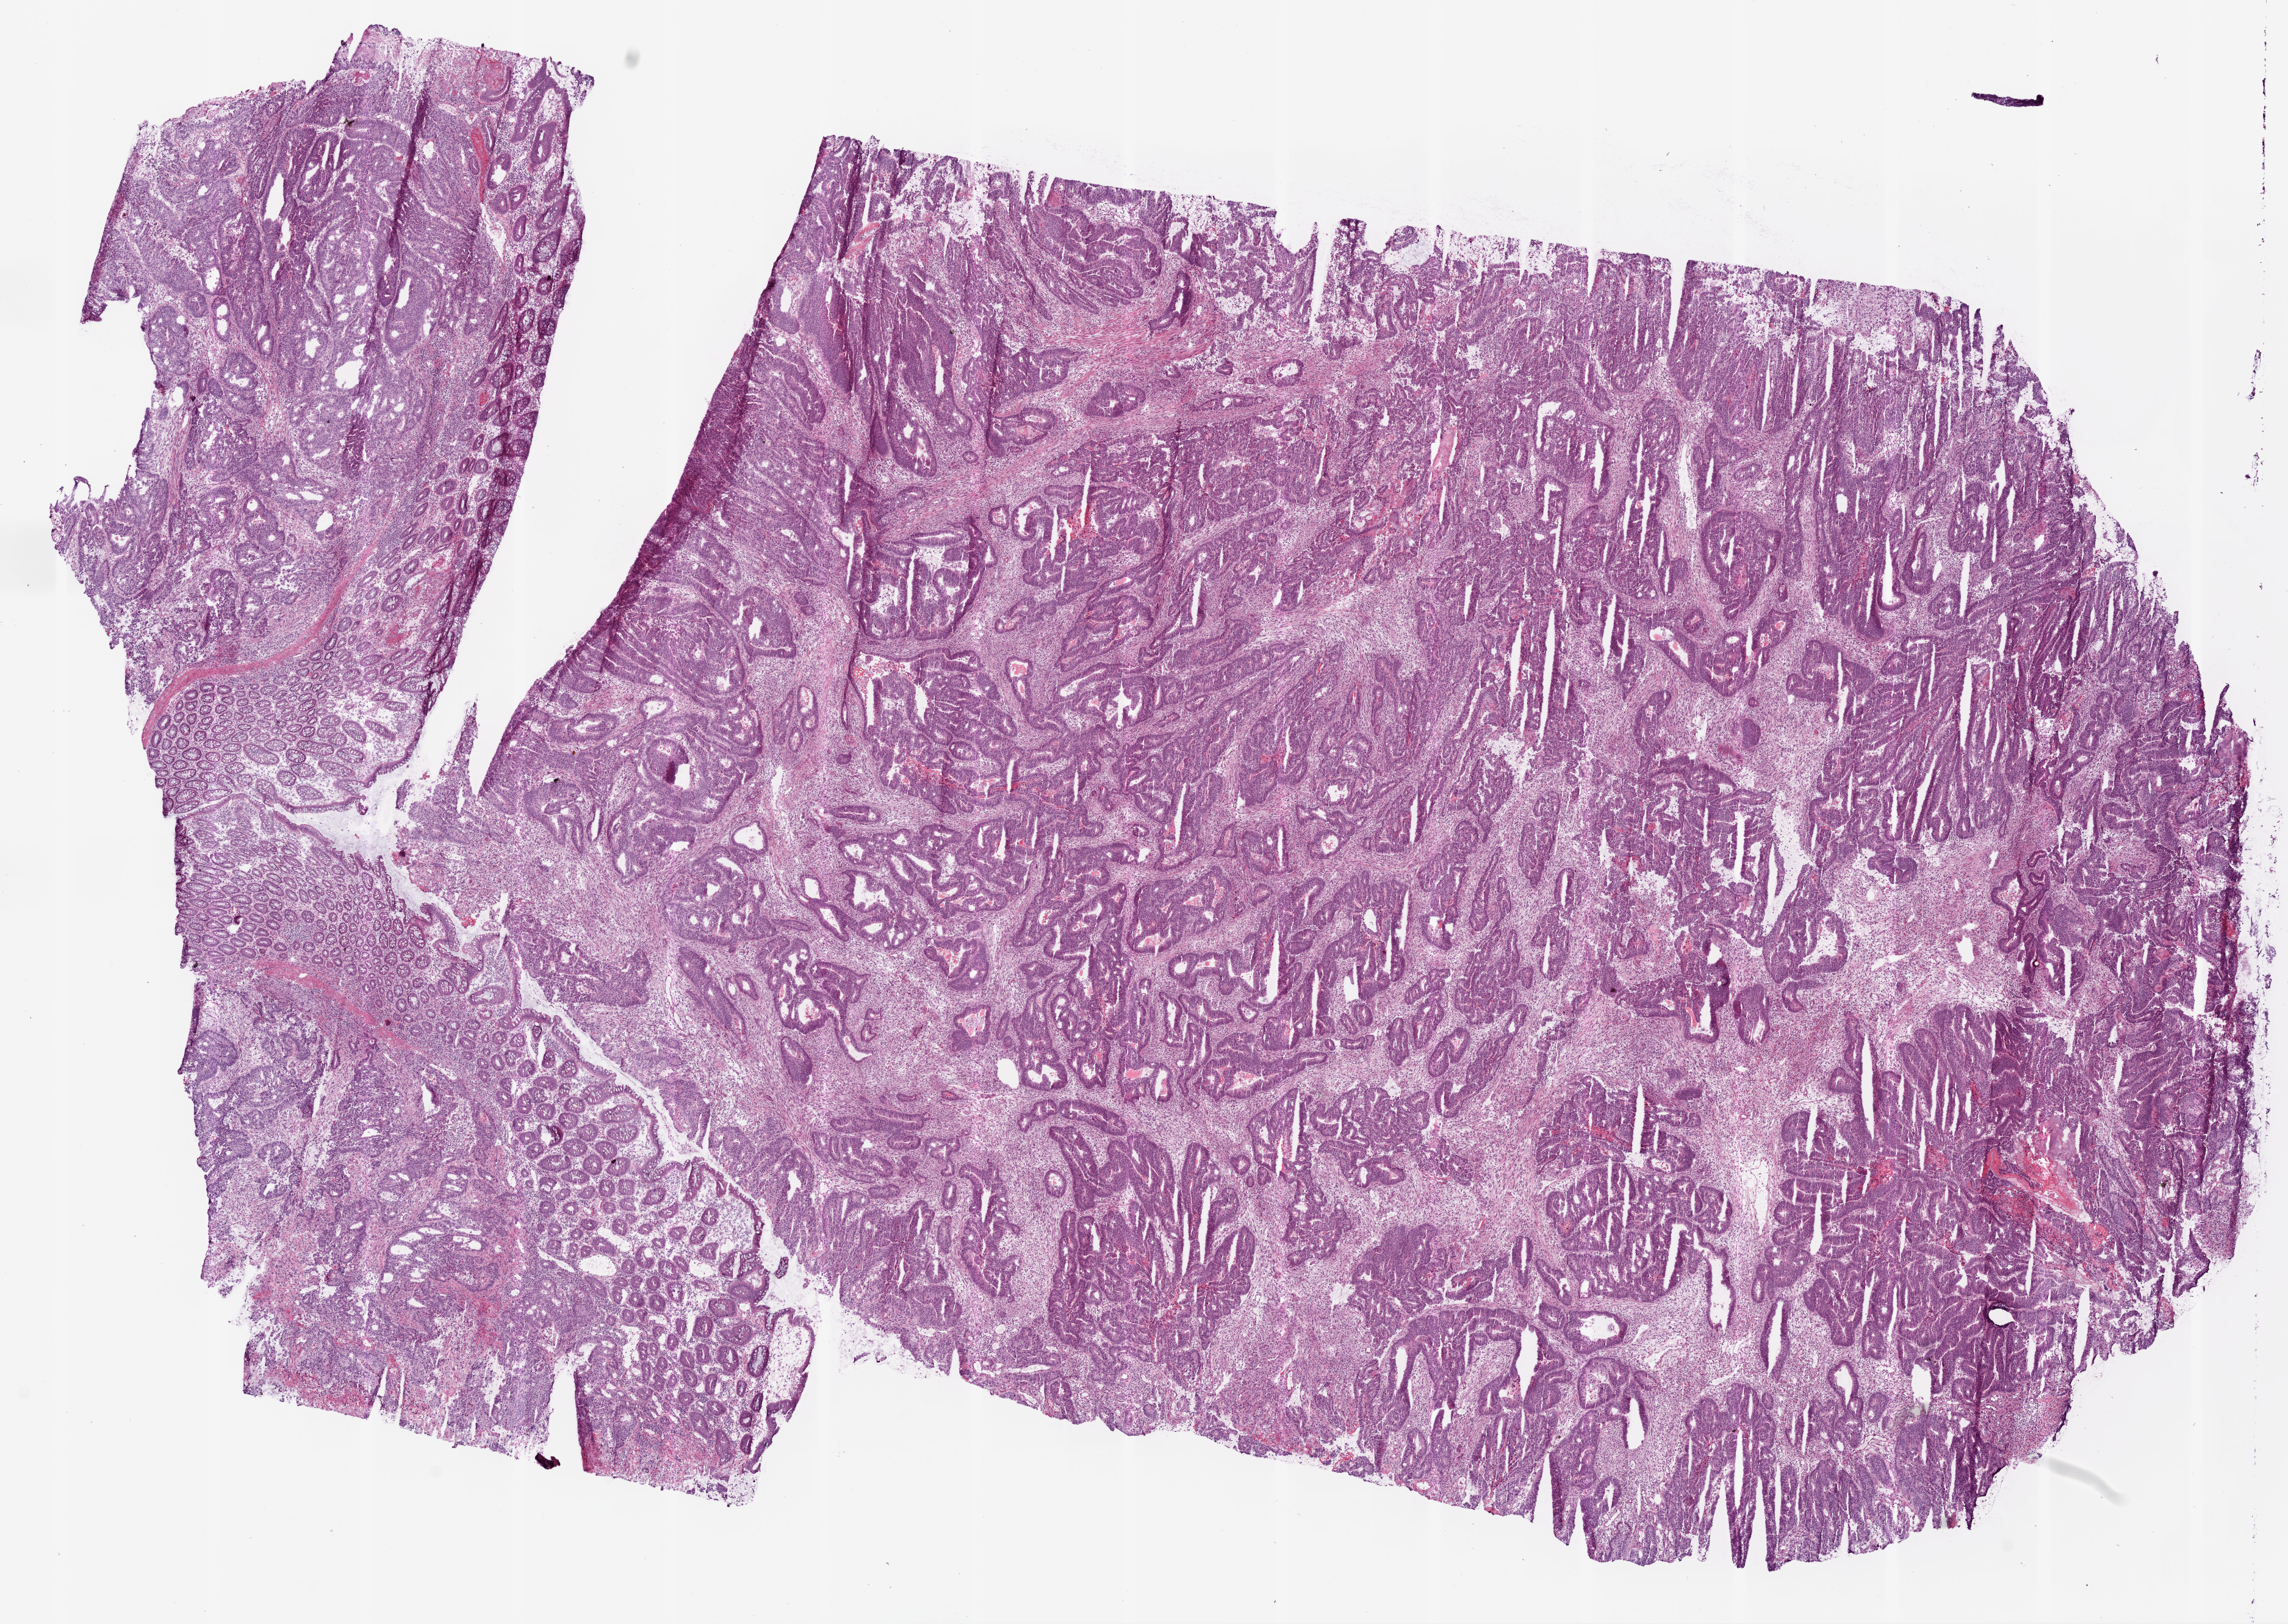
H&E-stained whole-slide image — whole scanned area (about 15.0 x 10.7 mm) shown as a low-resolution overview; frozen section; sample: primary tumour, colon. Patient: male, age at initial diagnosis 79 years. Pathologist review of this section (percent, as recorded): tumour cells 60%, tumour nuclei 65%, normal cells 10%, stromal cells 20%, necrosis 10%.
Lymph nodes positive (case pathology): 0 of 19 examined. Histologic diagnosis: Adenocarcinoma, NOS (ascending colon). AJCC pathologic stage: IIA (7th edition).